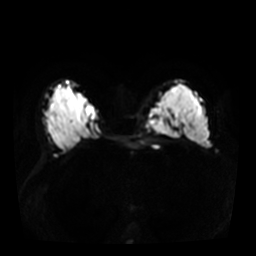
Breast MRI, one axial slice; slice 20 of 36 in the series (ordered by position); diffusion-weighted series; image 2 of 4 stored at this slice position (different b-values; order by instance number); 3 T; 256 × 256 image matrix. Female patient.
Structures marked on this image (expert manual segmentation):
- tumour on diffusion-weighted imaging: box from (x=150, y=100) to (x=175, y=137) px